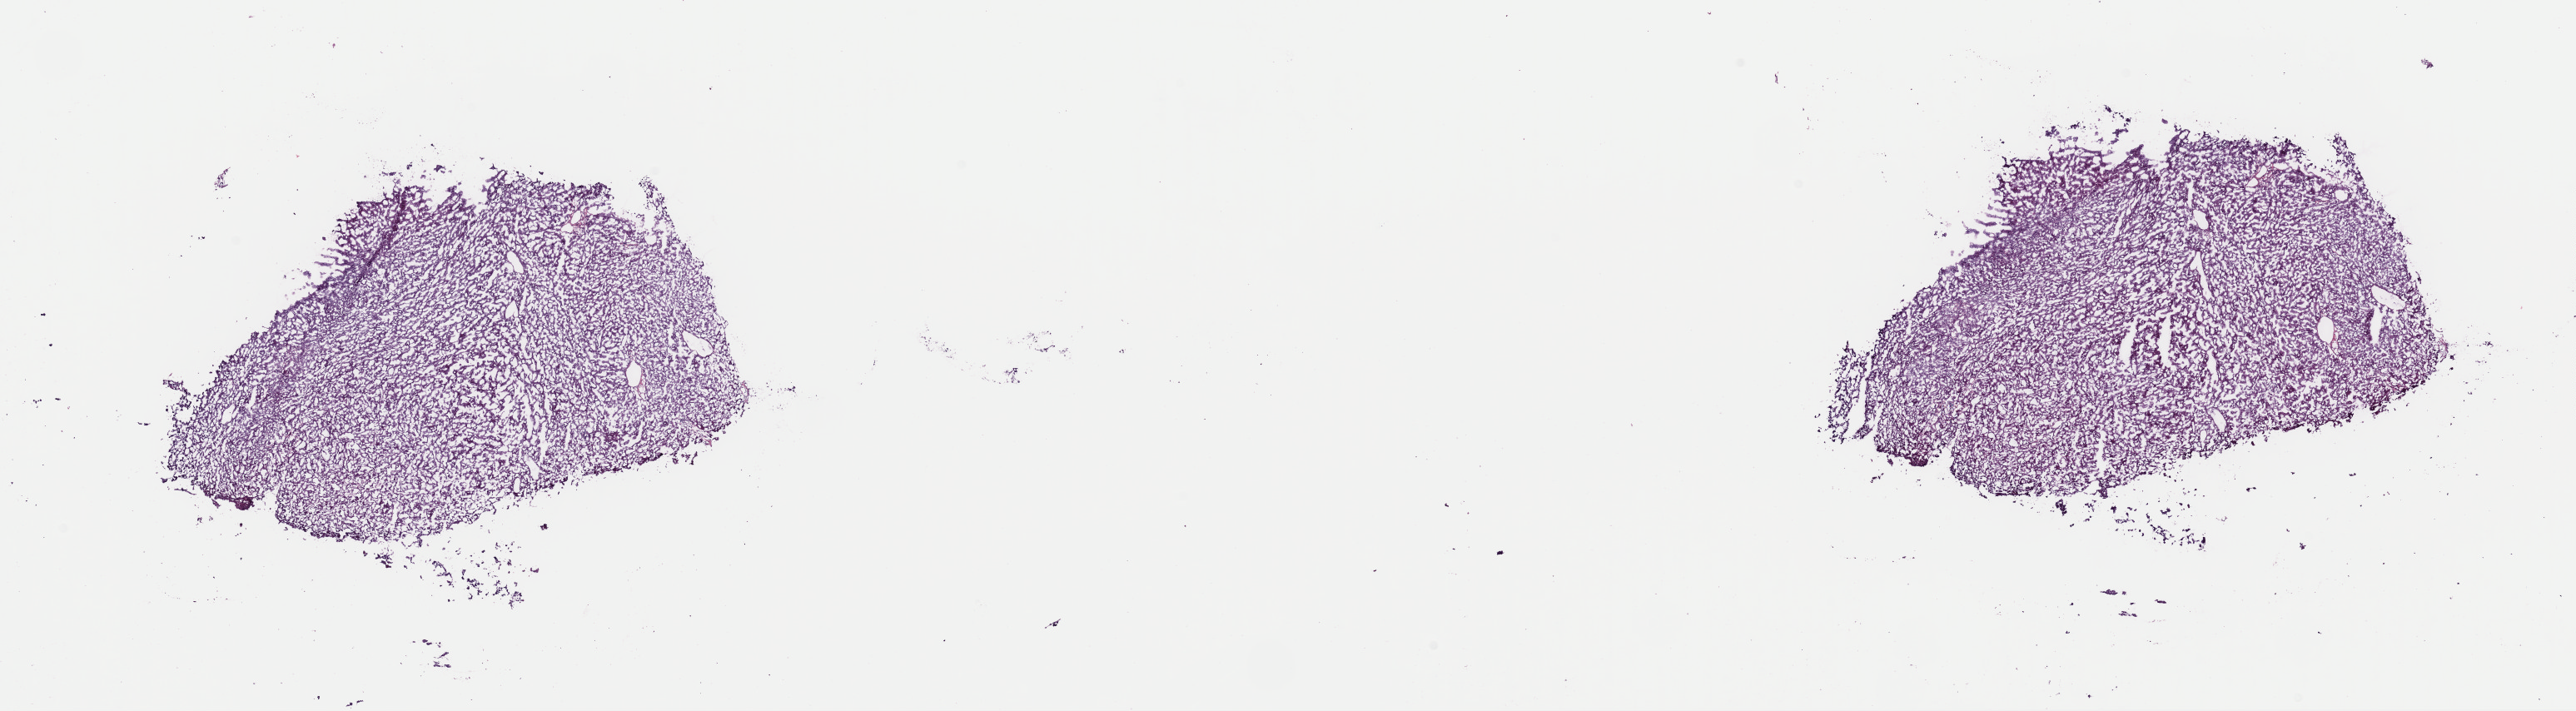
Whole-slide histology image, H&E — a low-resolution overview of the entire scanned area, about 24.4 x 6.7 mm. Frozen section from the top of the tissue portion. Primary tumour sample from the liver. Male patient; age at initial diagnosis 65 years. Histologic grade: G1 (well differentiated). Pathologist review of this section (percent, as recorded): tumour cells 100%, tumour nuclei 80%, normal cells 0%, stromal cells 0%, necrosis 0%. Inflammatory infiltration, as recorded: lymphocyte infiltration 1%, monocyte infiltration 0%, neutrophil infiltration 0%.
- diagnosis: Hepatocellular carcinoma, NOS
- AJCC pathologic stage: I